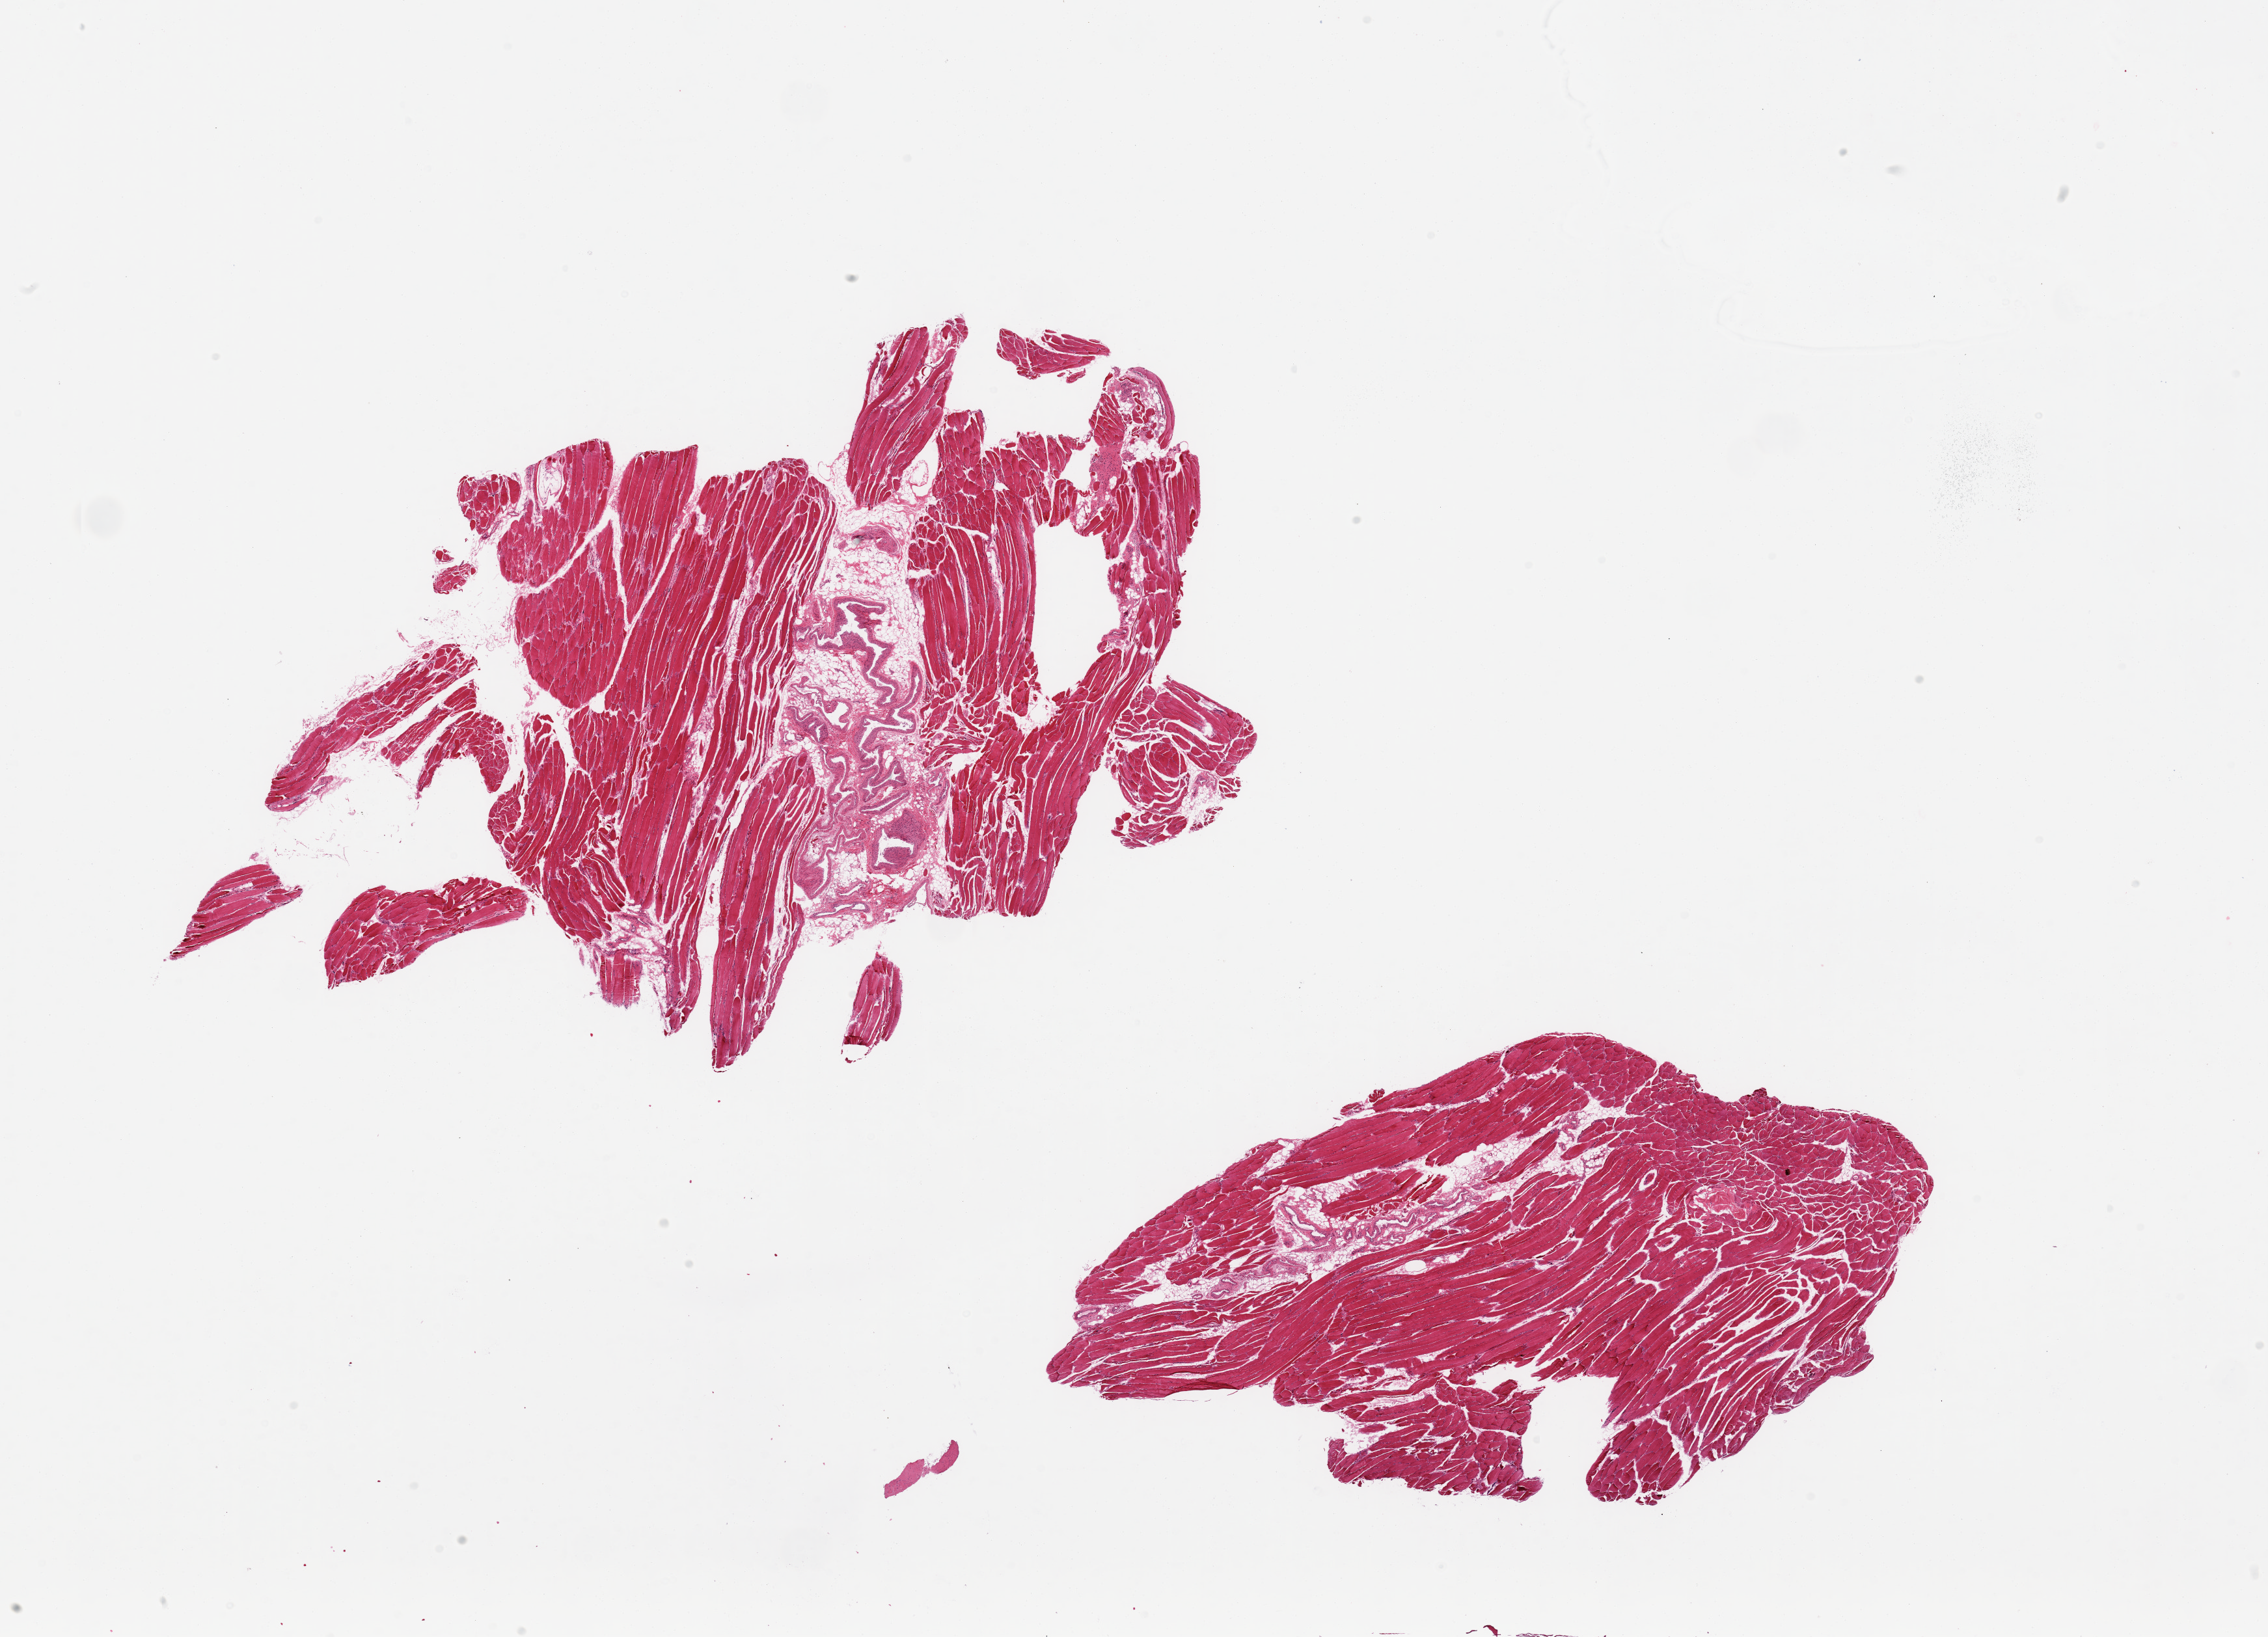
Digitized hematoxylin and eosin (H&E)-stained section — a low-resolution overview of the entire scanned area, about 27.6 x 19.9 mm (from a 20x scan). PAXgene-fixed paraffin-embedded (PFPE) section. Section of skeletal muscle (target tissue). Donor tissue sample.
• reviewer comment on this tissue sample: 2 pieces; 20% and 10% internal fibrovascular and fatty tissue